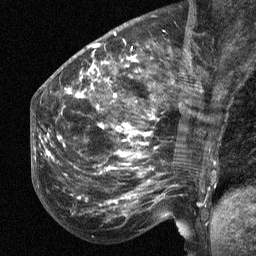
Breast MRI (dynamic contrast-enhanced), one sagittal slice; position 22 of 64 along the scan axis; dynamic contrast-enhanced study with each time point stored as its own series, time point 2 of 3 at this slice position (early post-contrast, ordered by acquisition time); 1.5 T; TE 4.8 ms, TR 27 ms; 2.3 mm slice thickness; 256 × 256 image matrix, field of view 200 × 200 mm. Female patient, age 50 years. From the clinical record (not read from this slice): setting: breast cancer imaged before/during neoadjuvant chemotherapy; receptor status: HER2-positive.
Annotated regions visible in this slice (semi-automatically segmented with operator editing):
- analysis volume of interest (the breast-tissue region the enhancement analysis was run in; not a lesion): bounding box <53,64,211,218> (left, top, right, bottom; pixels)
- tumour enhancement mask (voxels above the 90 % enhancement threshold inside the analysis volume of interest): <67,70,155,202>